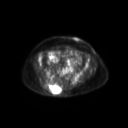
FDG PET of an extremity soft-tissue mass (from a PET/CT study), one axial slice; slice 75 of 267 in the series (ordered by position); 128 × 128 image matrix. Patient: female, 60 years. Case-level facts recorded for this patient, not image findings: histological type: spindle cell suggestive of myxofibrosarcoma; grade: intermediate; site of the primary tumour: right buttock.
Structures marked on this image (expert contour drawn on MRI and transferred to this co-registered scan by the dataset authors):
- gross tumour volume (mass): bounding box <42,83,63,95> (left, top, right, bottom; pixels)